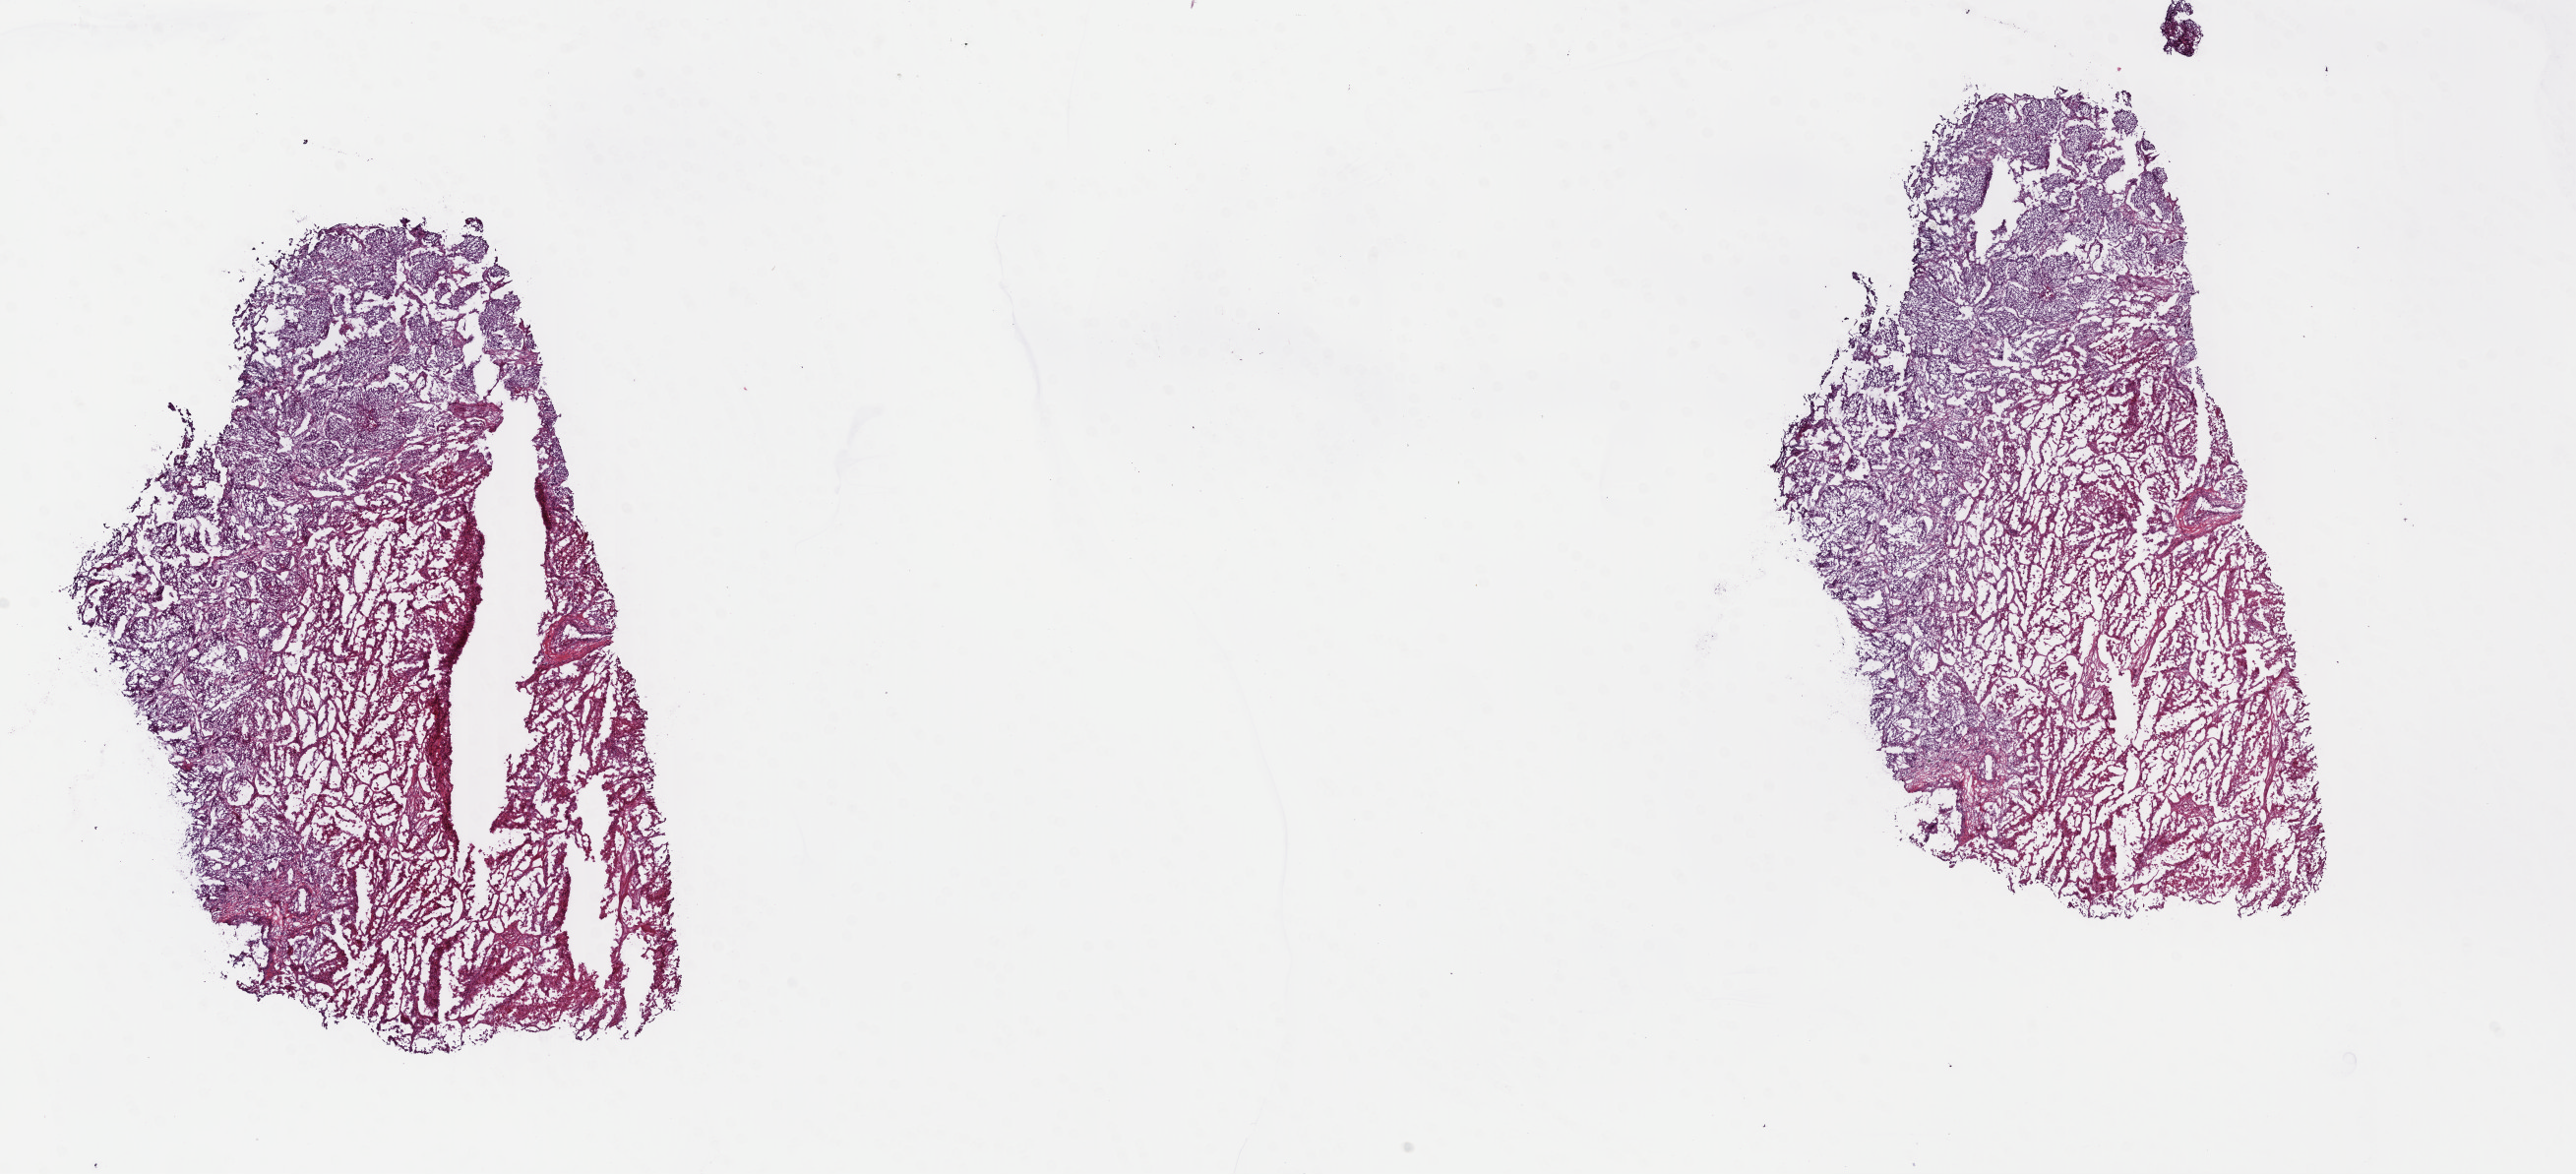
Whole-slide histology image, H&E-stained, low-resolution overview of the scanned area, about 20.6 x 9.4 mm; frozen section; primary tumour sample from the lung. Male patient; age at initial diagnosis 80 years. Pathologist review of this section (percent, as recorded): tumour cells 50%, tumour nuclei 65%, normal cells 50%, stromal cells 0%, necrosis 0%. Inflammatory infiltration, as recorded: lymphocyte infiltration 0%, monocyte infiltration 0%, neutrophil infiltration 0%.
• AJCC pathologic stage: IIB (7th edition)
• diagnosis: Squamous cell carcinoma, NOS (lower lobe, lung)
• laterality: right